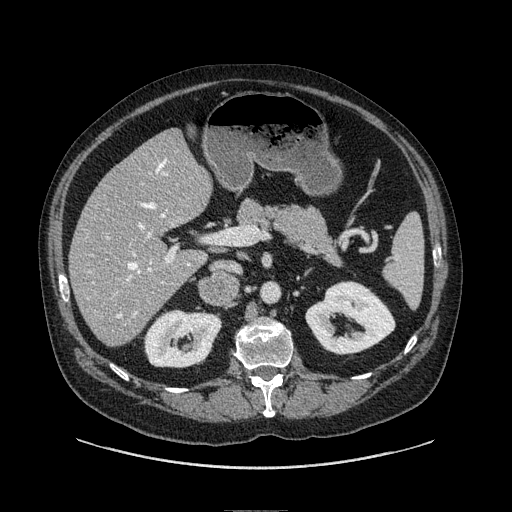
Contrast-enhanced abdominal CT, one axial slice. Slice 39 of 149 in the series (ordered by position). Soft-tissue window (W 400 / L 40 HU). 1.25 mm slice thickness. 512 × 512 image matrix, field of view 440 × 440 mm. Male patient. From the clinical record (not read from this slice): diagnosis: adrenocortical carcinoma; tumour side: right adrenal; tumour size at pathology: 7.5 cm; Ki-67 index: 15 %; stage (as recorded): 2.
Structures marked on this image (semi-automatically segmented with operator editing):
- mass: bounding box (x1, y1, x2, y2) in pixels: (201, 272, 237, 303)